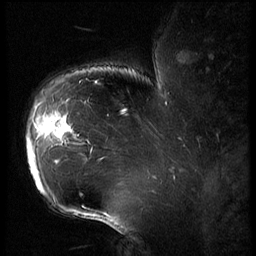
Breast MRI (dynamic contrast-enhanced), one sagittal slice. Slice 48 of 62 in the series (ordered by position). 3 images stored at this slice position (order not interpretable as contrast timing). 1.5 T. TE 4.2 ms, TR 9 ms. 2.5 mm slice thickness. 256 × 256 image matrix, field of view 180 × 180 mm. Female patient, age 43 years. From the clinical record (not read from this slice): setting: breast cancer imaged before/during neoadjuvant chemotherapy; receptor status: HER2-positive.
Outlined on this slice (semi-automatic segmentation, software-assisted and operator-edited):
- analysis volume of interest (the breast-tissue region the enhancement analysis was run in; not a lesion): box from (x=25, y=90) to (x=82, y=203) px
- tumour enhancement mask (voxels above the 140 % enhancement threshold inside the analysis volume of interest): (x=27, y=112)–(x=77, y=190)